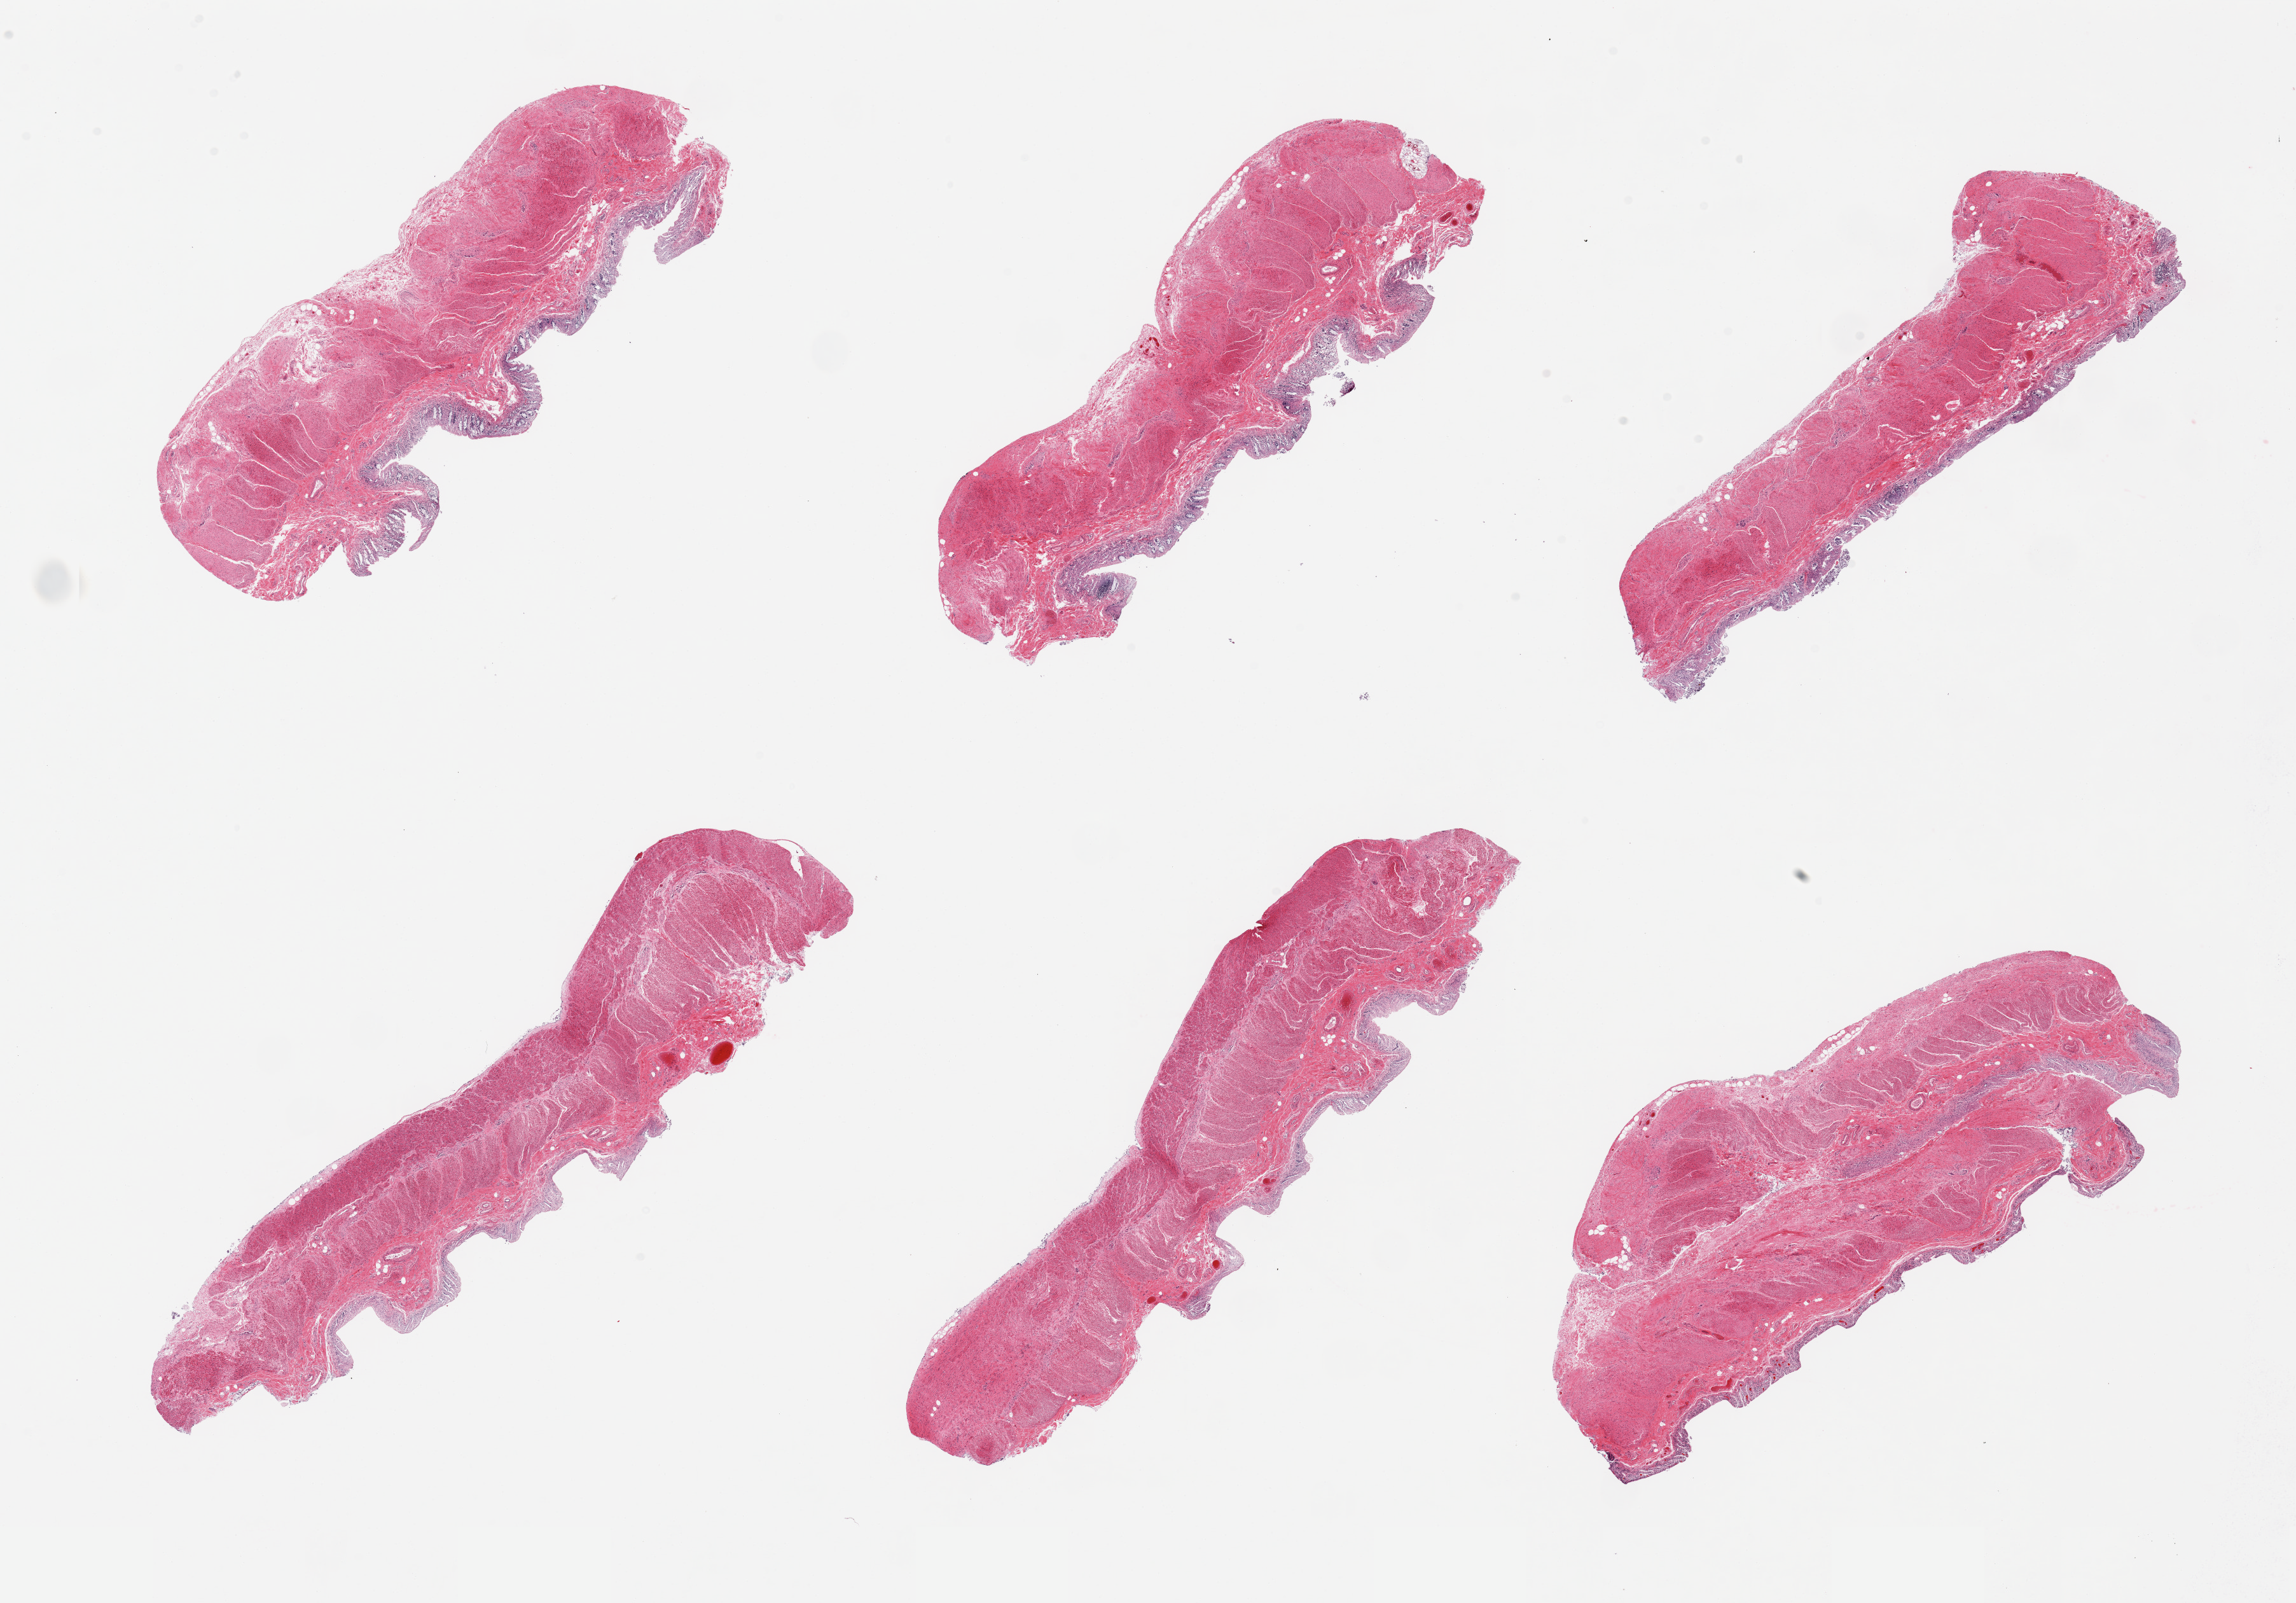
Whole-slide image, hematoxylin and eosin (H&E) stain — low-resolution overview of the scanned area, about 28.5 x 19.9 mm, PAXgene-fixed paraffin-embedded (PFPE) section, section of transverse colon (target tissue), tissue donor sample. Female donor.
Pathologist's review note for this sample: 6 pieces; full thickness sections, moderate to severe autolysis.